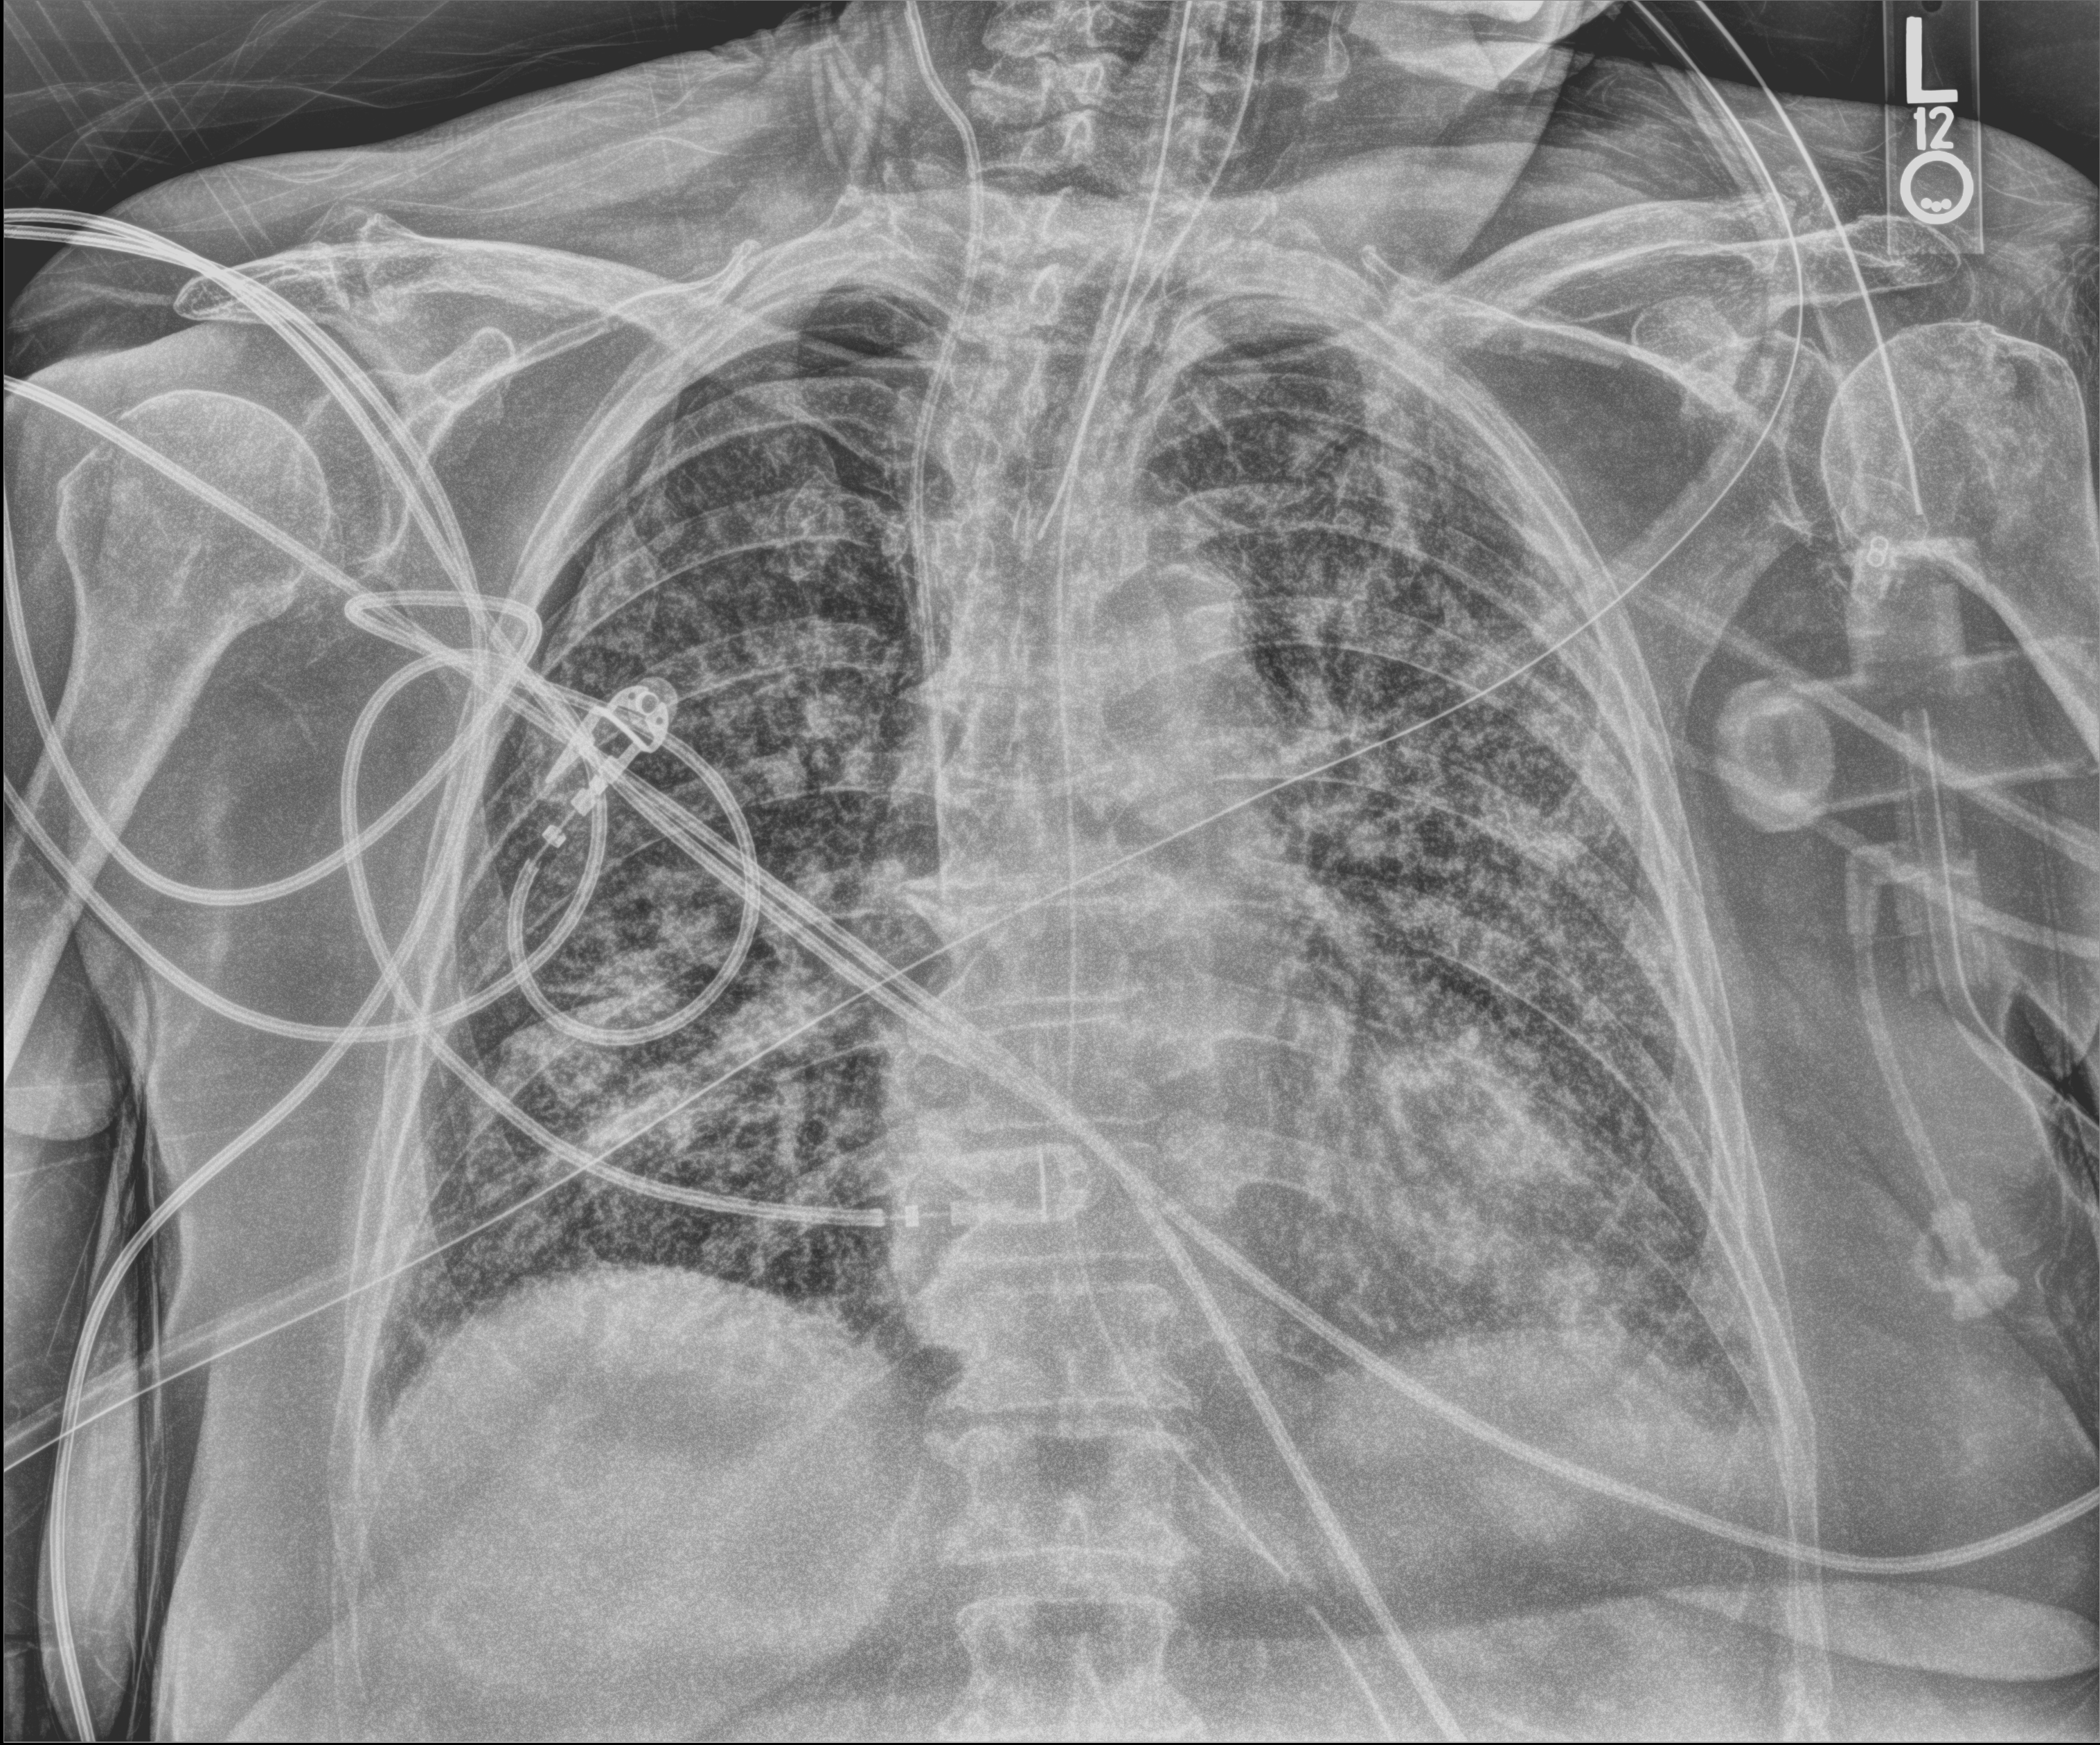
Bedside chest radiograph (digital radiography), anteroposterior (AP) projection. Female patient hospitalised with COVID-19, age 75–90 years.
From the hospital-stay record, not from the radiograph (when in the stay this image was taken is not recorded): admitted to intensive care during this hospital stay: no.